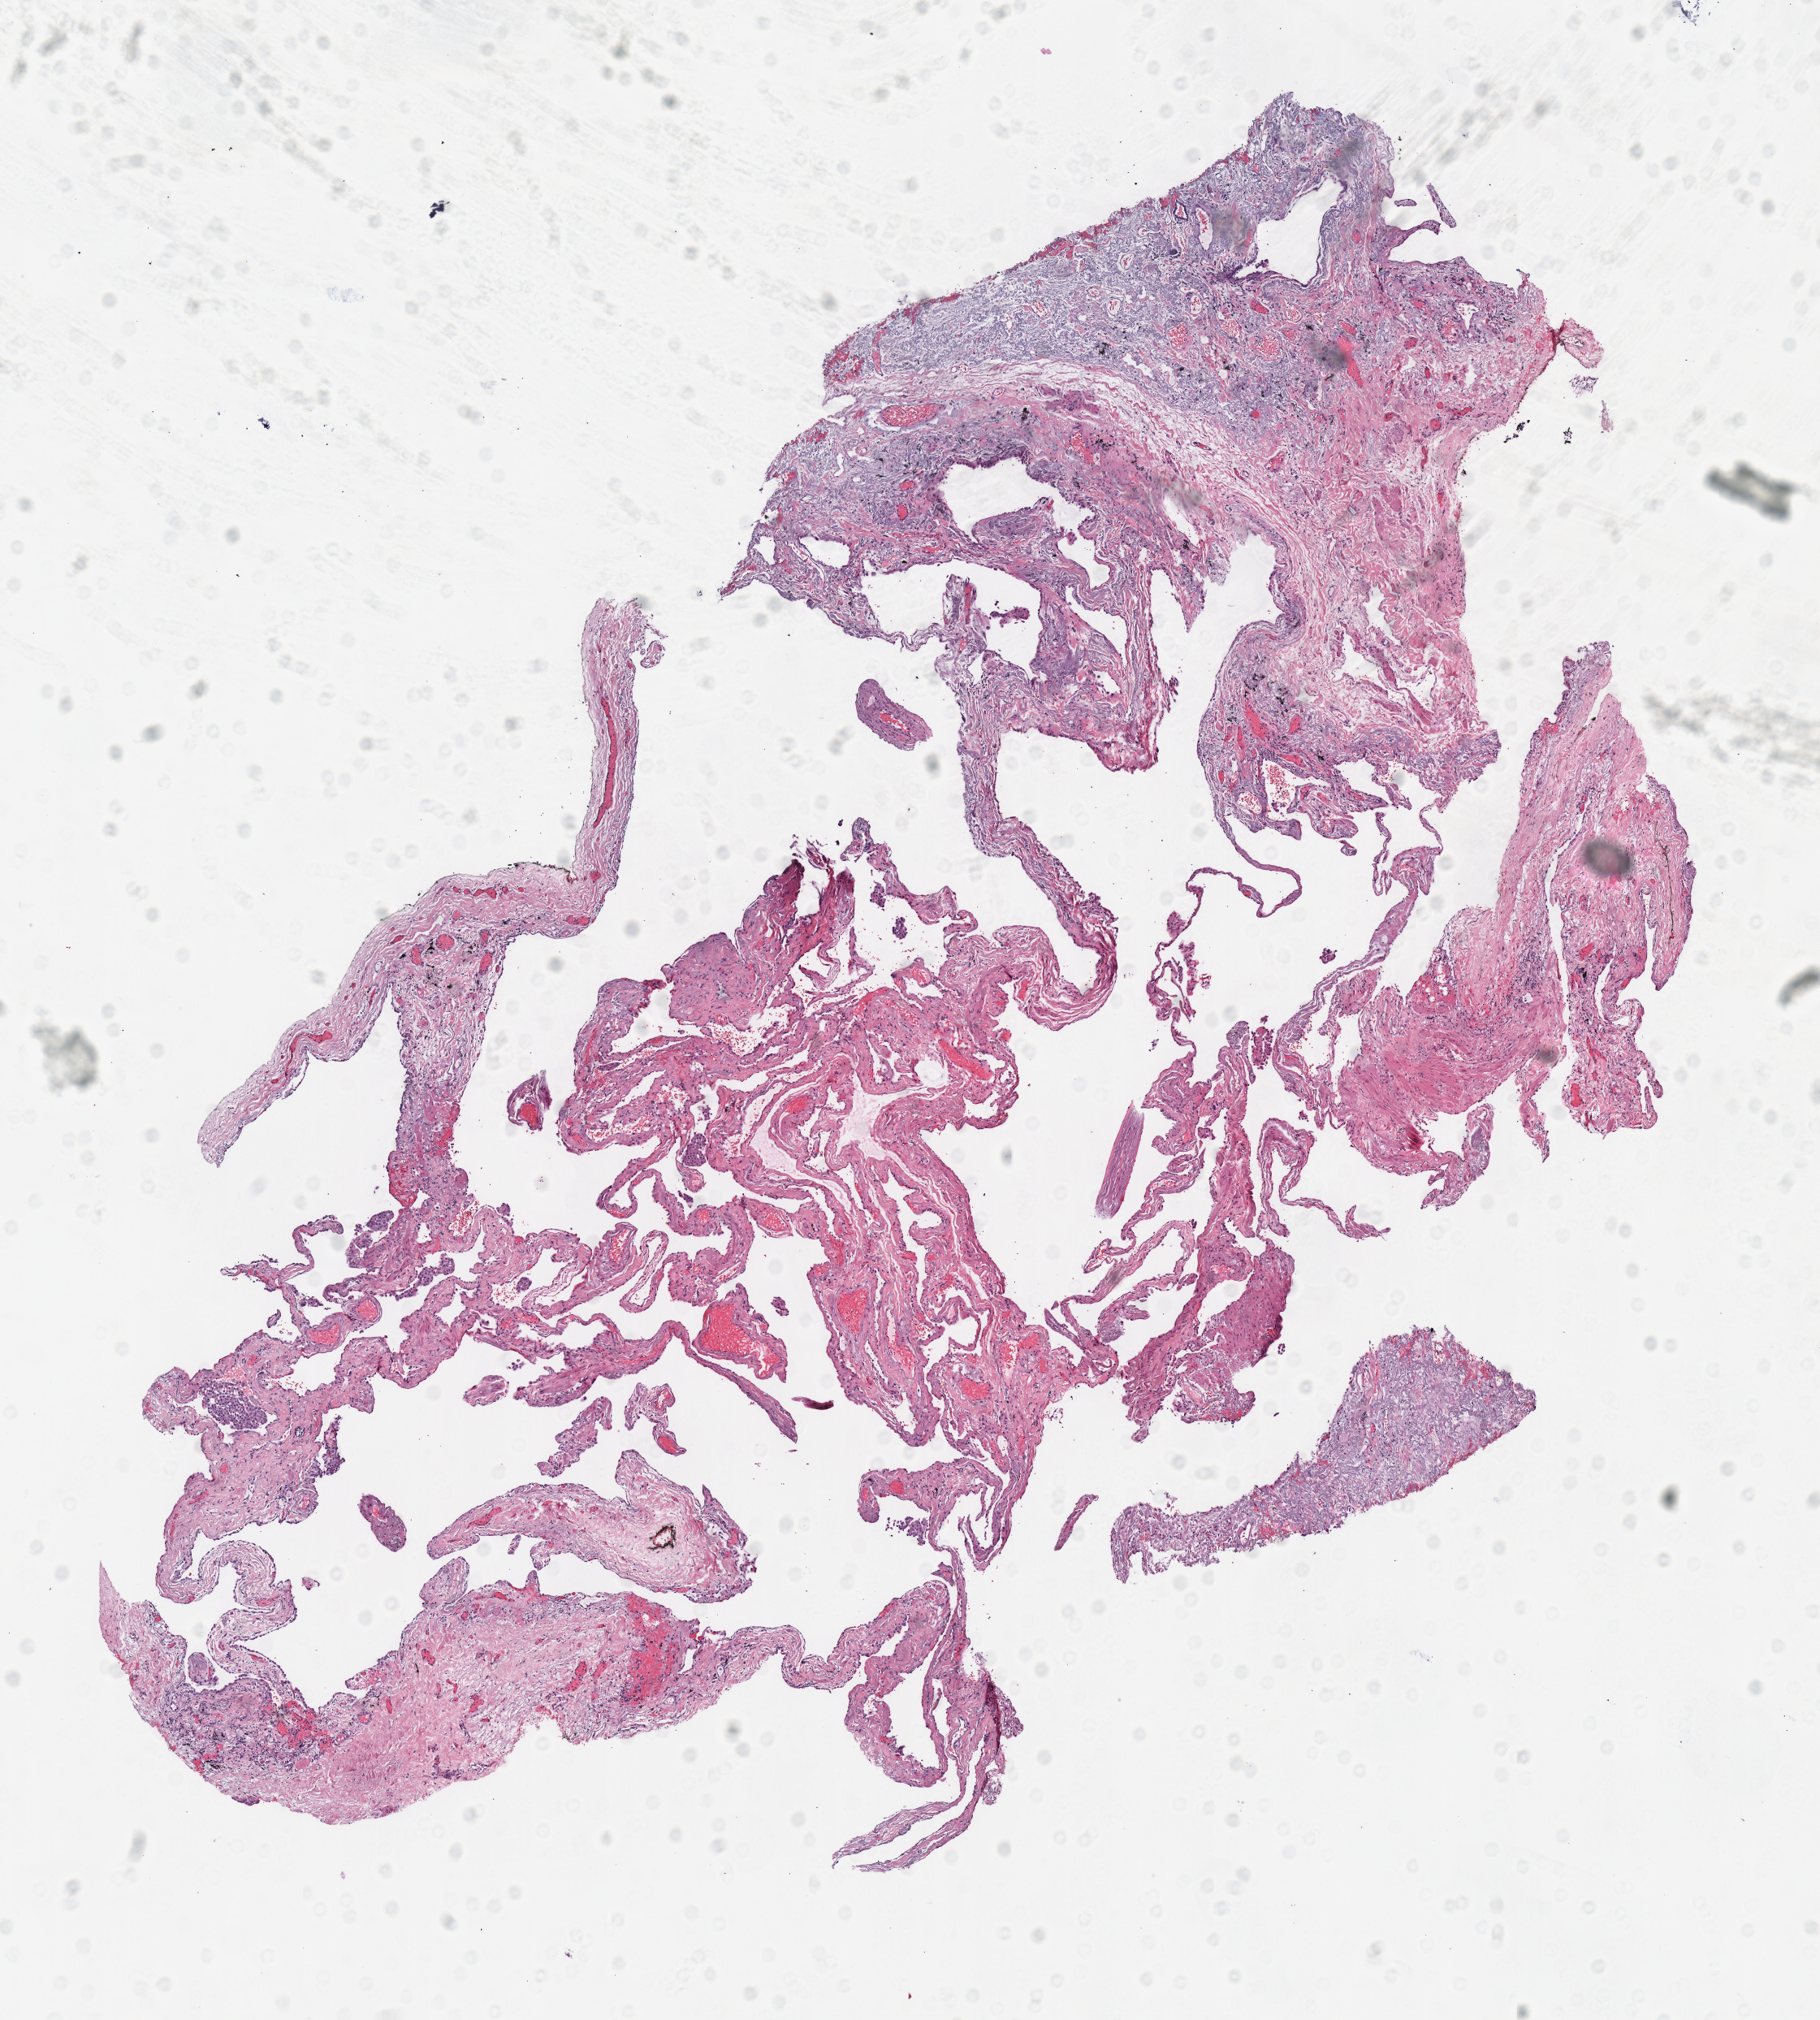
Whole-slide histology image, H&E, low-resolution overview of the scanned area, about 8.8 x 9.8 mm (acquisition: 40x scan). Frozen section from the top of the tissue portion. Sample: solid tissue normal (non-tumour tissue), lung. Female, age 68 years at initial diagnosis.
• this section: solid tissue normal (non-tumour) sample from the same patient
• patient diagnosis: Squamous cell carcinoma, NOS